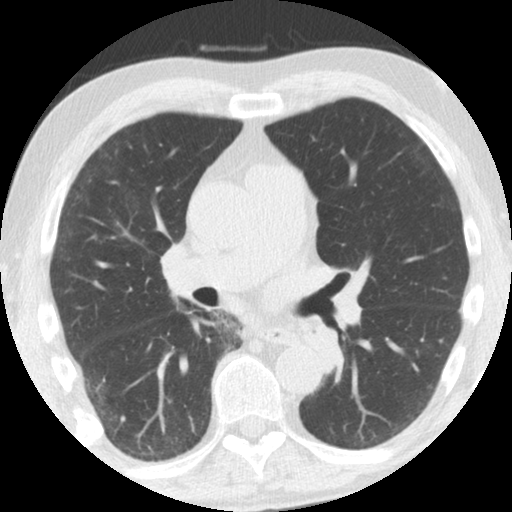
Axial slice from a low-dose chest CT screening exam; third screening round (two years after baseline); lung window (W 1500 / L -600 HU); 2.5 mm slice thickness. Male participant, aged 61 years at enrolment. Former smoker at enrolment.
Lesion marked by an expert reader, bounding box [x1, y1, x2, y2] px = [294, 316, 344, 362]. Screening reader's record for this exam: no non-calcified nodule ≥4 mm recorded. Lung cancer was diagnosed 363 days after this screen: squamous cell carcinoma, NOS, left upper lobe, left lower lobe, well differentiated (G1), stage IIB (AJCC 6th edition), 100 mm at pathology.